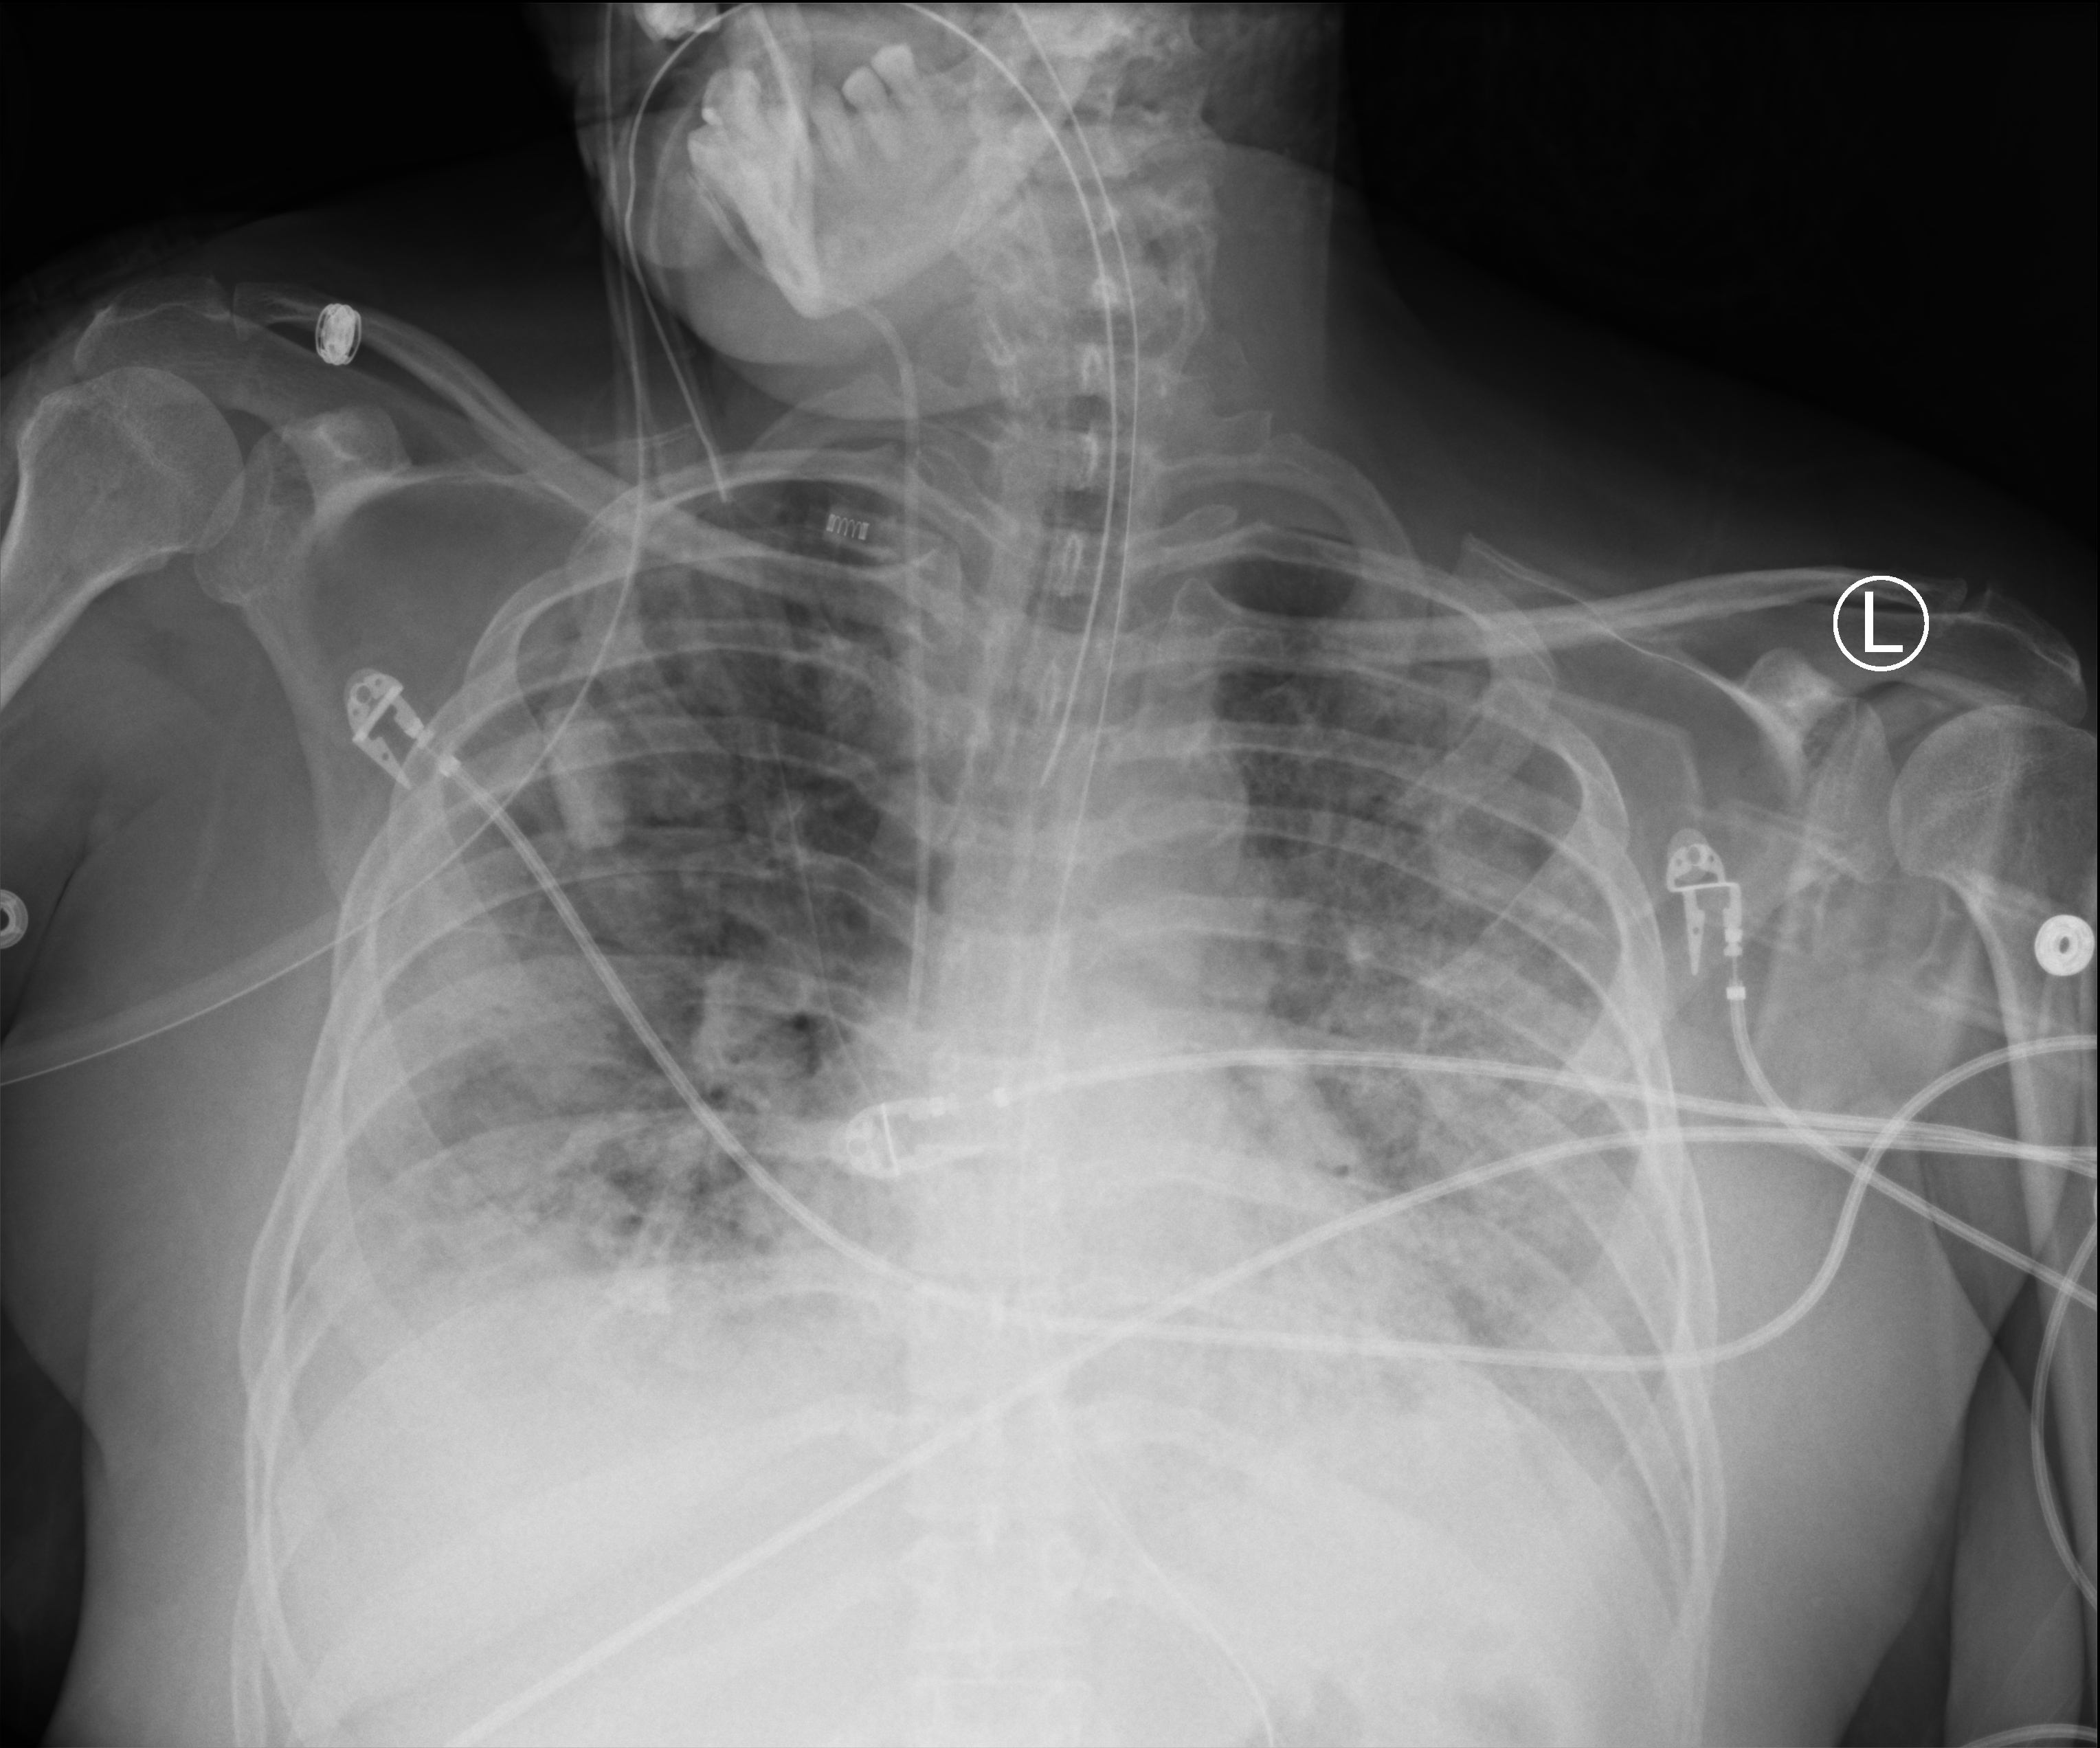
Bedside chest radiograph (computed radiography), anteroposterior (AP) projection. Adult patient hospitalised with COVID-19, age 18–59 years.
From the hospital-stay record, not from the radiograph (when in the stay this image was taken is not recorded): length of hospital stay: 15 days.